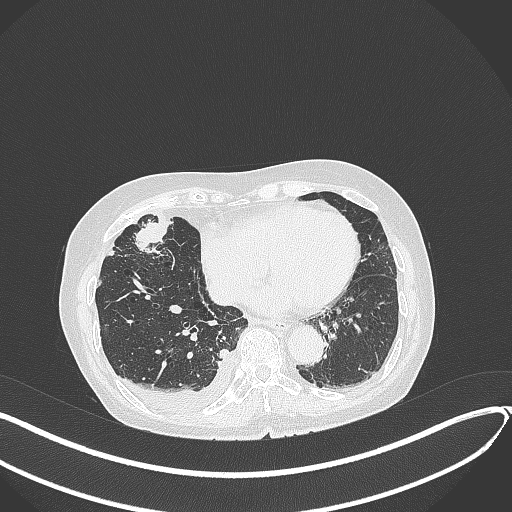
Chest CT, one axial slice. Position 128 of 418 along the scan axis. Reconstruction kernel B70f. 120 kVp. Lung window (W 1500 / L -600 HU). 1 mm slice thickness. 512 × 512 image matrix, field of view 400 × 400 mm. Patient: female, 75 years. Case-level facts recorded for this patient, not image findings: clinical TNM (as recorded): T2a N3 M0.
Annotated regions visible in this slice (bounding box drawn by a radiologist):
- lung tumour (recorded histology: adenocarcinoma): bounding box <133,216,169,260> (left, top, right, bottom; pixels)